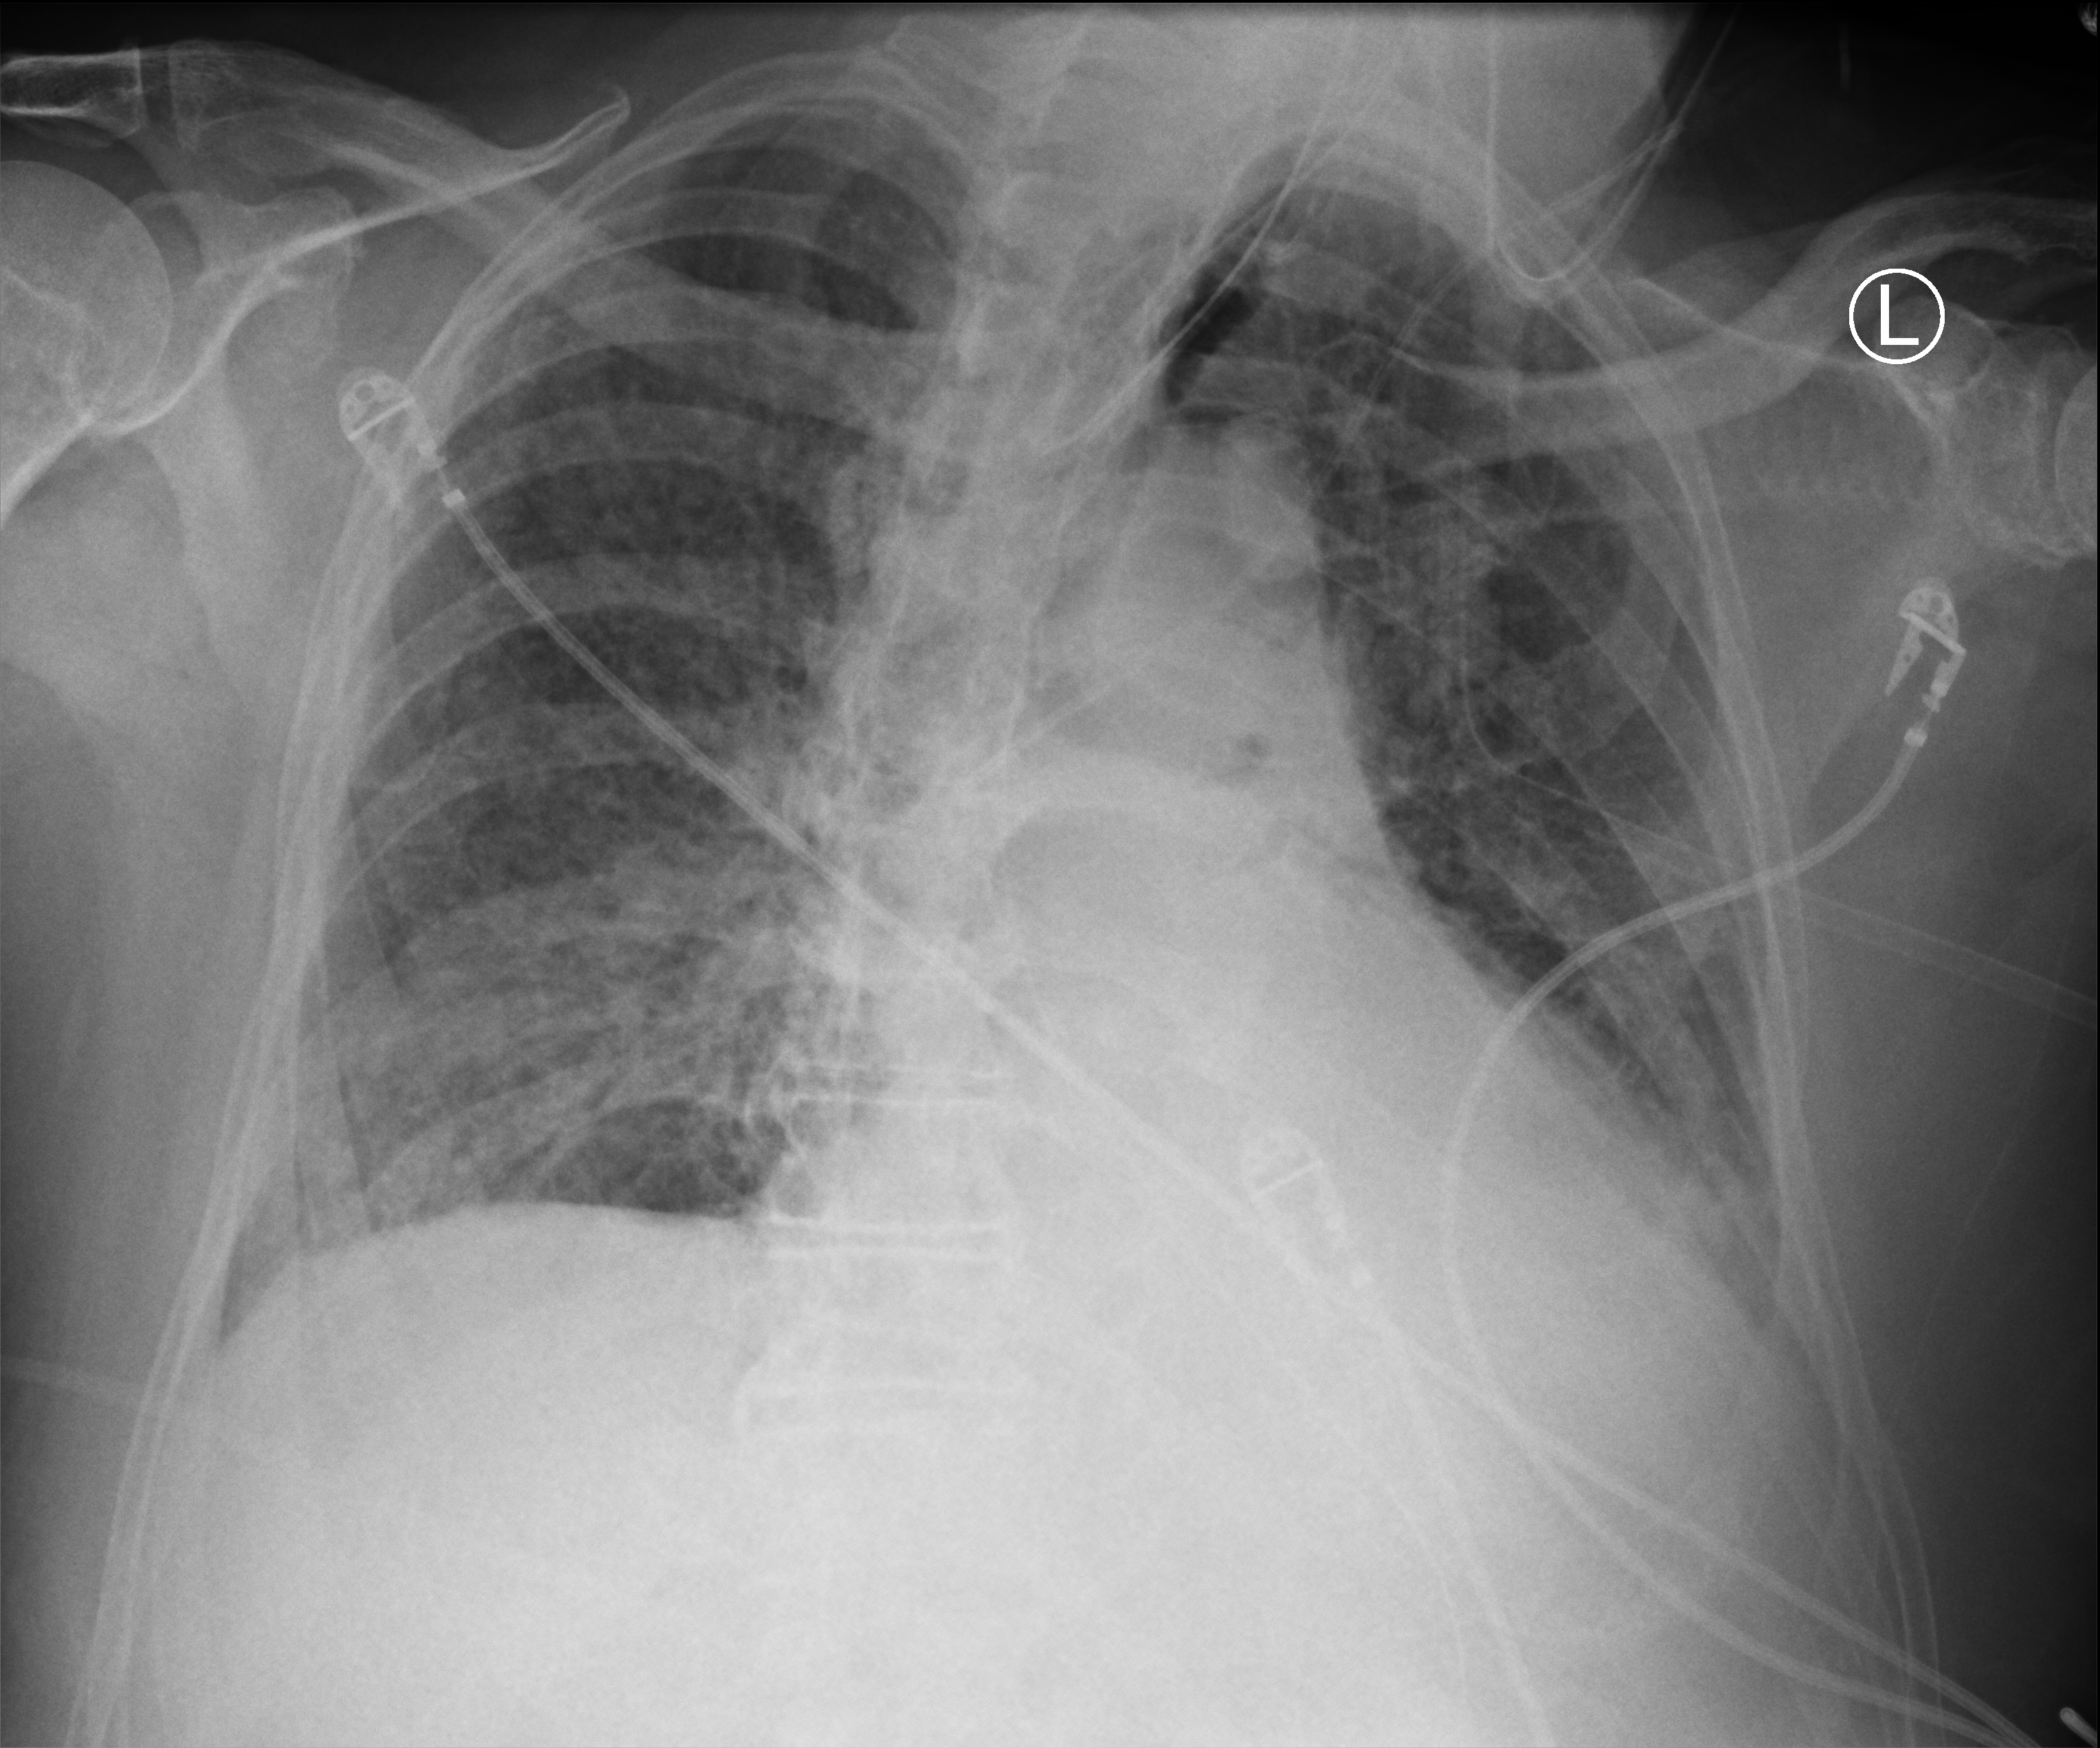
Chest X-ray (portable); anteroposterior (AP) projection. Patient hospitalised with COVID-19; male, aged 75–90 years.
Hospital-stay facts (about this admission, not read from this image; timing relative to this image not recorded): smoking status (admission record): former.